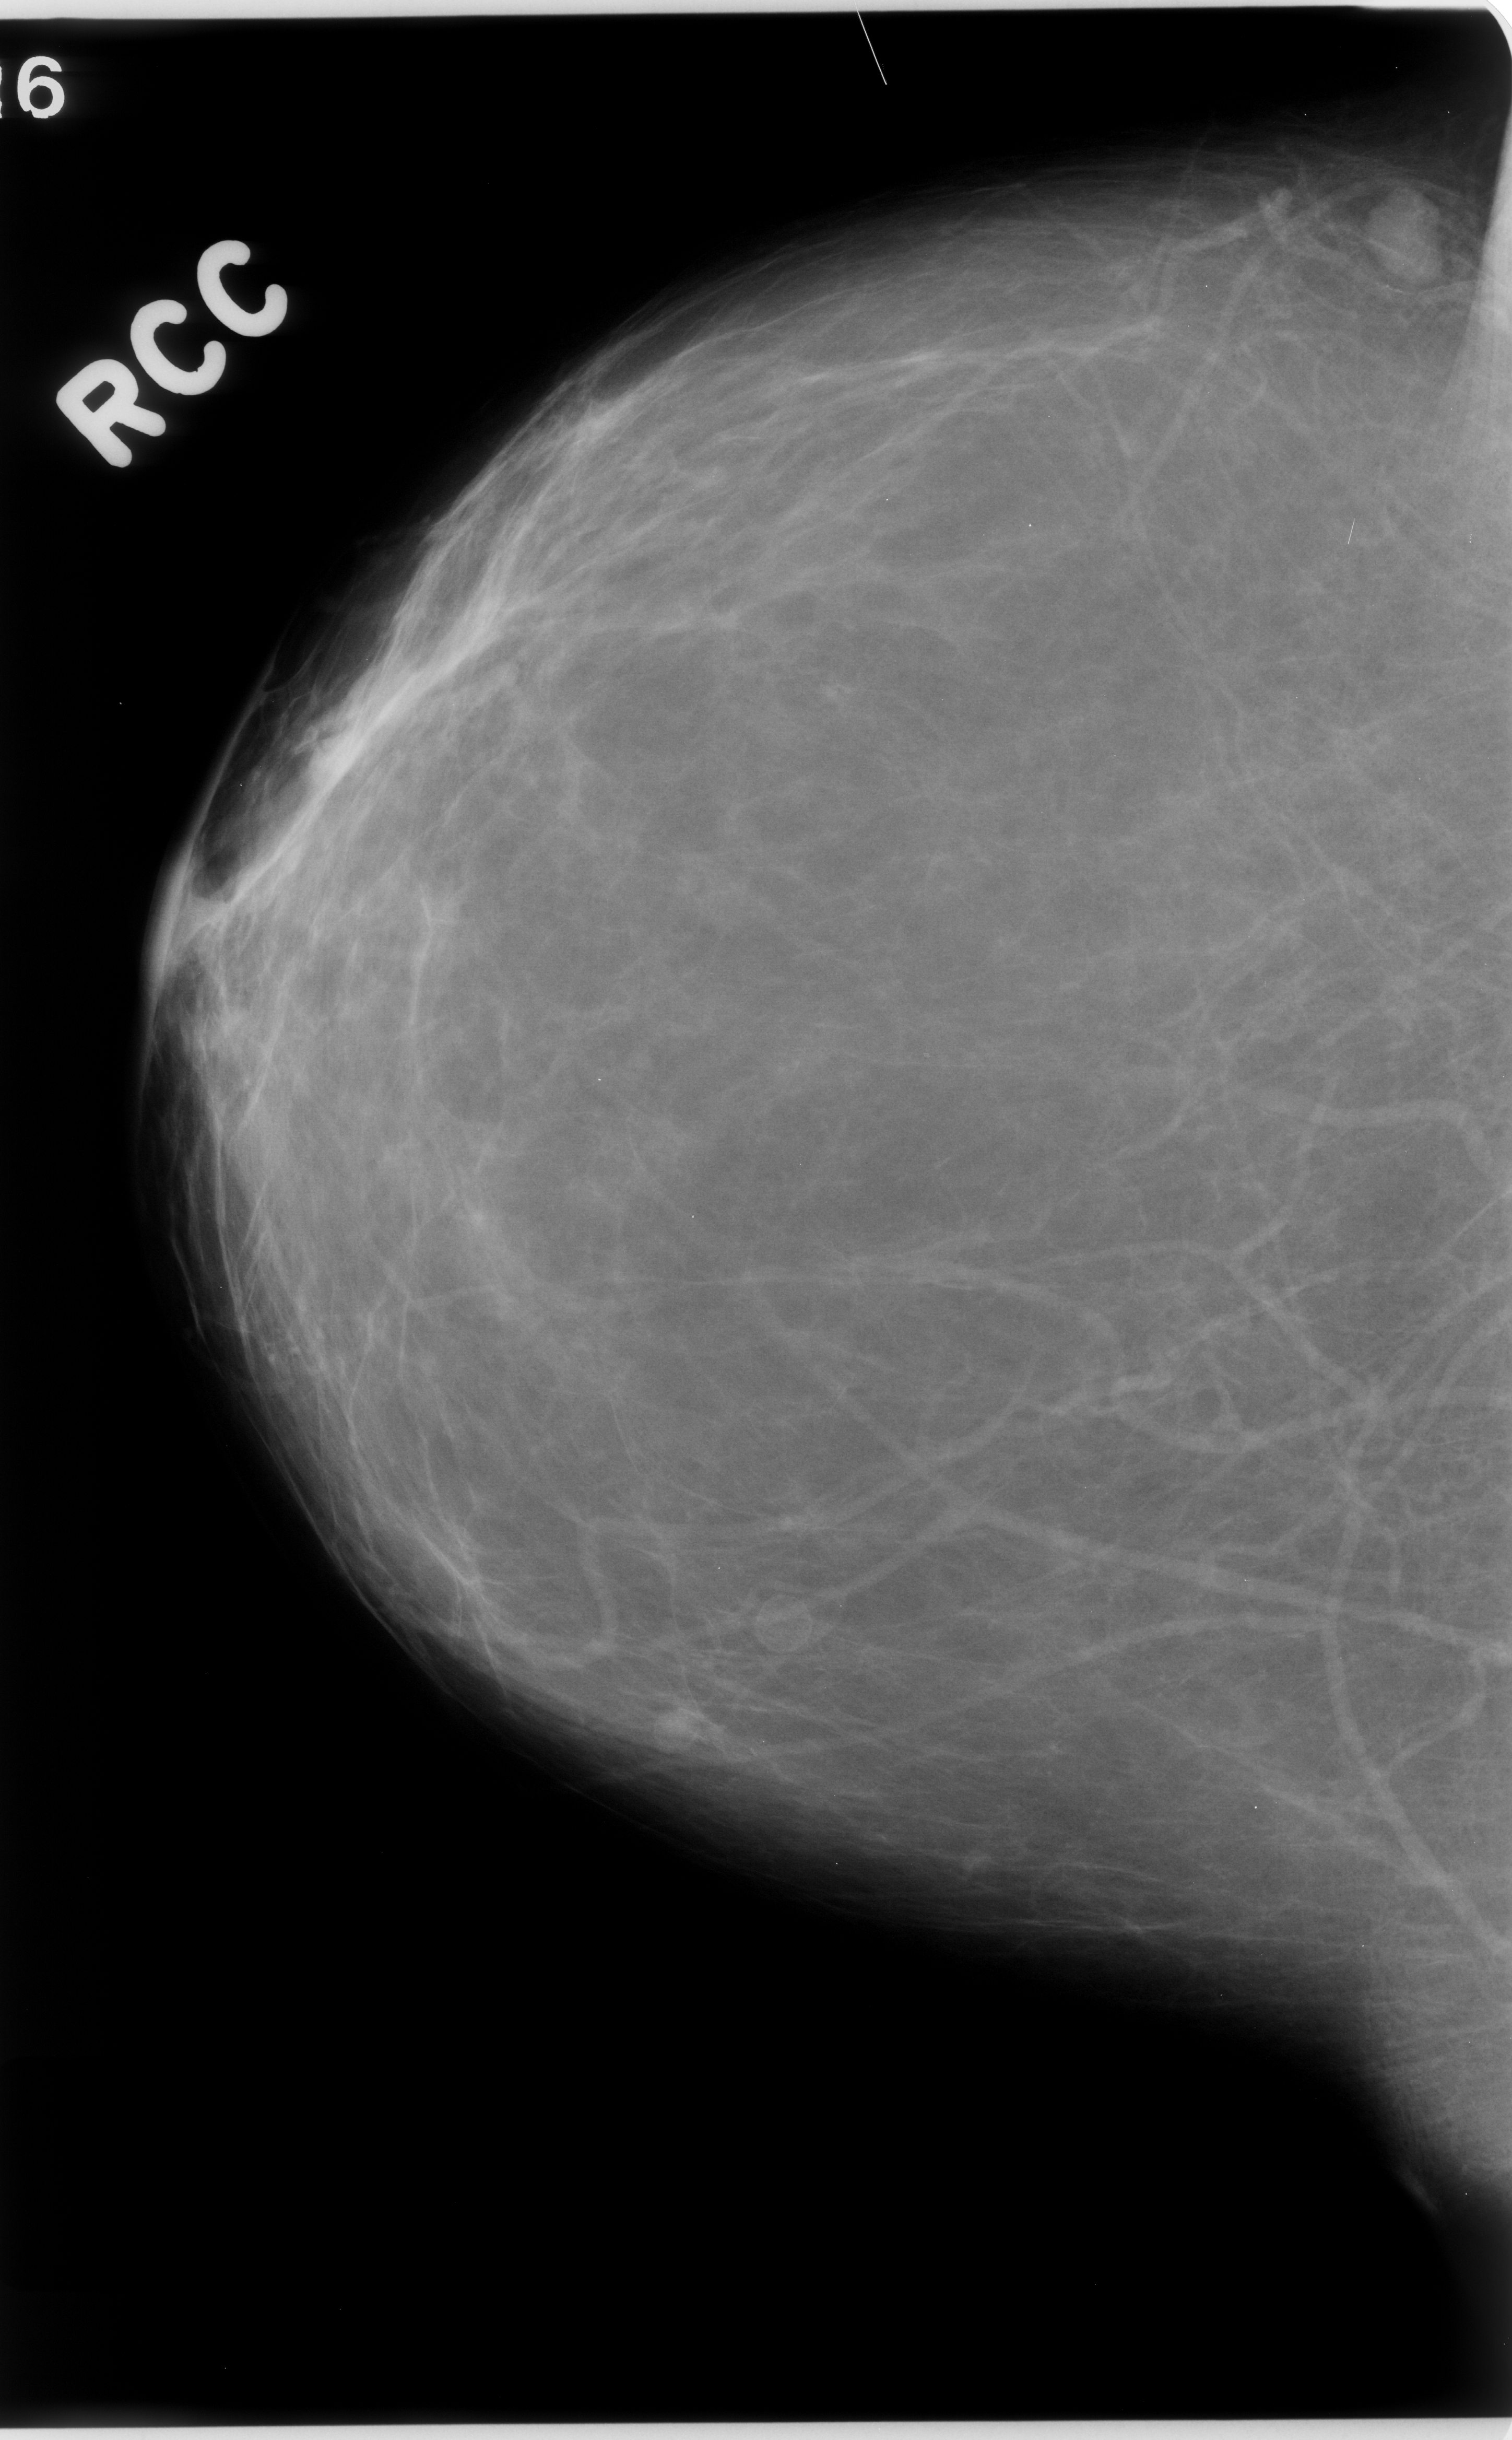
Digitized screen-film mammogram. Right breast. CC view. Breast composition: almost entirely fatty (BI-RADS density category 1 of 4). 1512 × 2440 image matrix.
Expert-marked regions of interest on this image (one box per marked abnormality):
- mass, shape oval, margins circumscribed; BI-RADS assessment category 3; pathology (as recorded): benign: bounding box <1340,160,1458,285> (left, top, right, bottom; pixels)